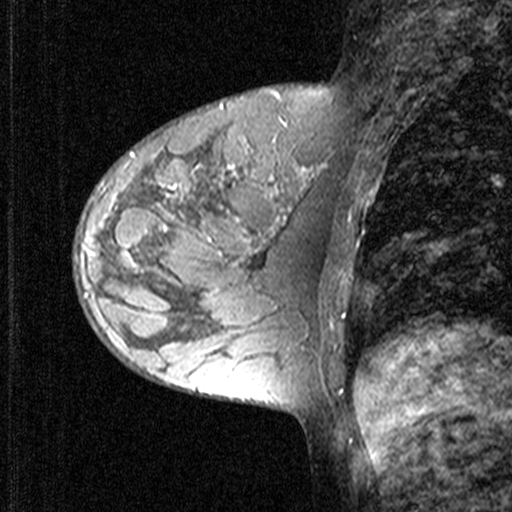
Breast MRI (dynamic contrast-enhanced), one sagittal slice; dynamic contrast-enhanced study with each time point stored as its own series, time point 2 of 3 at this slice position (early post-contrast, ordered by acquisition time); 1.5 T; TE 4.5 ms, TR 11 ms; 512 × 512 image matrix. Patient: female, 27 years. Case-level facts recorded for this patient, not image findings: setting: breast cancer imaged before/during neoadjuvant chemotherapy; receptor status: HR-positive, HER2-negative.
Outlined on this slice (semi-automatic segmentation, software-assisted and operator-edited):
- analysis volume of interest (the breast-tissue region the enhancement analysis was run in; not a lesion): box from (x=74, y=146) to (x=165, y=239) px
- tumour enhancement mask (voxels above the 90 % enhancement threshold inside the analysis volume of interest): (x=130, y=153)–(x=136, y=156)